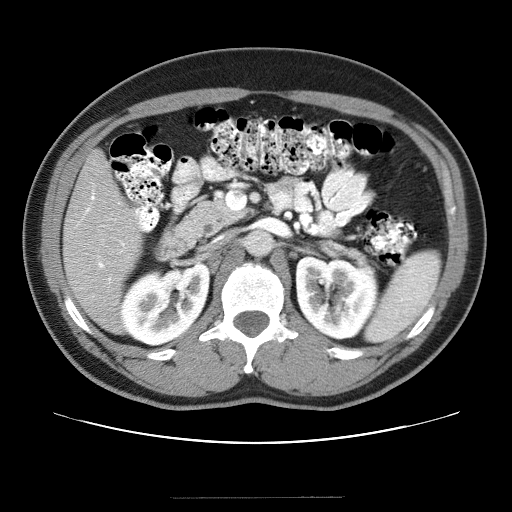
Contrast-enhanced abdominal CT (liver protocol), one axial slice. Position 12 of 40 along the scan axis. Soft-tissue window (W 400 / L 40 HU). 5 mm slice thickness. 512 × 512 image matrix, field of view 380 × 380 mm. From the clinical record (not read from this slice): diagnosis: hepatocellular carcinoma (patient treated with transarterial chemoembolisation; whether this scan precedes or follows treatment is not stated here); TNM stage (as recorded): Stage-IVA; Child-Pugh class: B; tumour nodularity: multinodular.
Outlined on this slice (semi-automatic segmentation, software-assisted and operator-edited):
- liver parenchyma outside the tumour (the mass and vessels are separate outlines, so this box may not span the whole liver): bounding box <62,150,142,330> (left, top, right, bottom; pixels)
- liver vessels: <78,191,125,282>